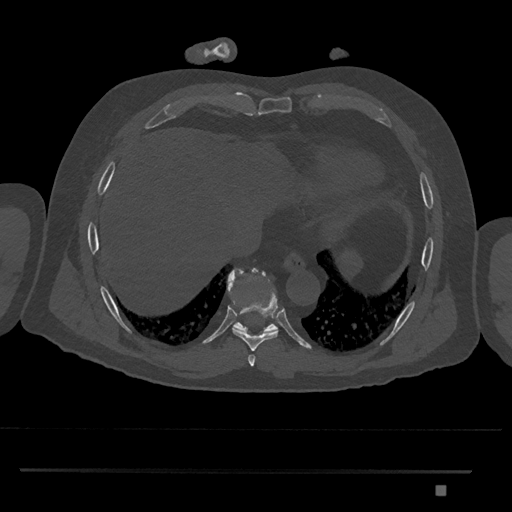
CT including the spine, one axial slice; slice 1091 of 1134 in the series (ordered by position); reconstruction kernel Br40s/3; 120 kVp; bone window (W 1800 / L 400 HU); 0.5 mm slice thickness; 512 × 512 image matrix. Patient: male, 65 years. From the clinical record (not read from this slice): primary cancer: prostate.
Outlined on this slice (semi-automatic segmentation, software-assisted and operator-edited):
- T8 vertebra: box from (x=232, y=271) to (x=278, y=351) px
- T9 vertebra: (x=227, y=268)–(x=278, y=333)